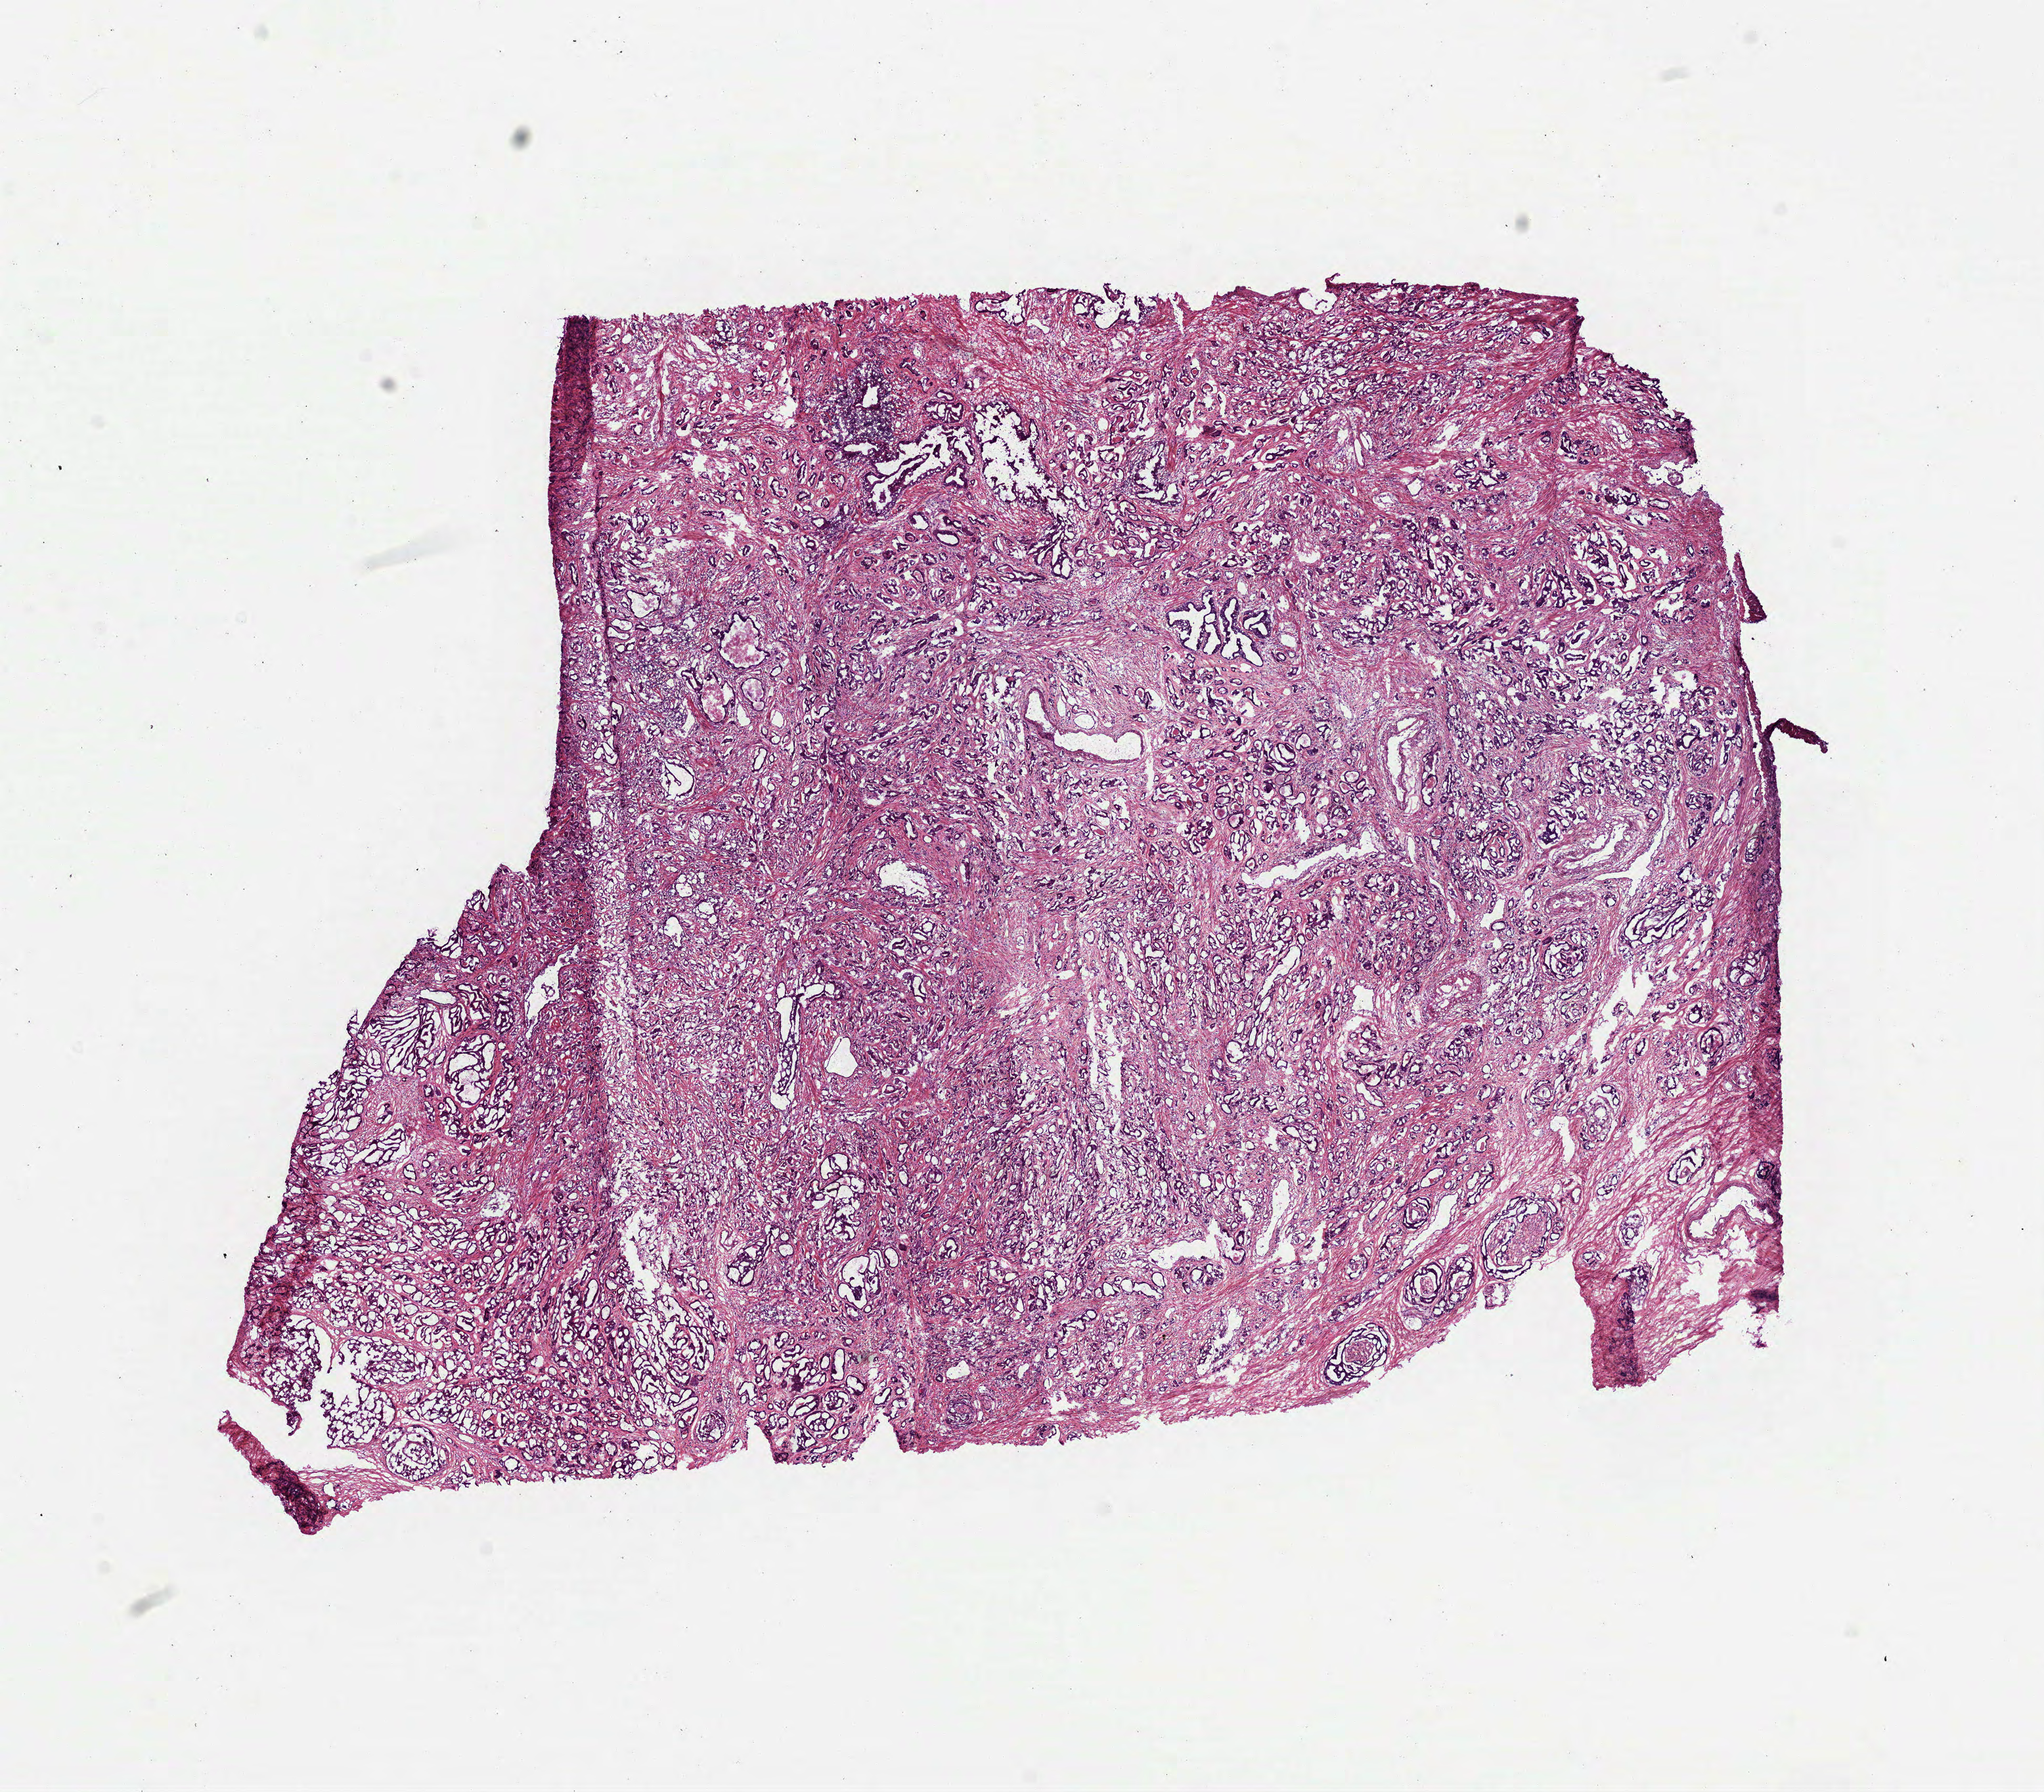
Digitized Hematoxylin and eosin (H&E) stained tissue section (whole slide) — shown as a low-resolution overview of the whole scanned area (about 12.5 x 11.0 mm); frozen section; primary tumour sample from the prostate. Male patient; age at initial diagnosis 61 years. Composition of this section per pathologist review: tumour cells 70%, tumour nuclei 70%.
Histologic diagnosis: Acinar cell carcinoma (prostate gland).